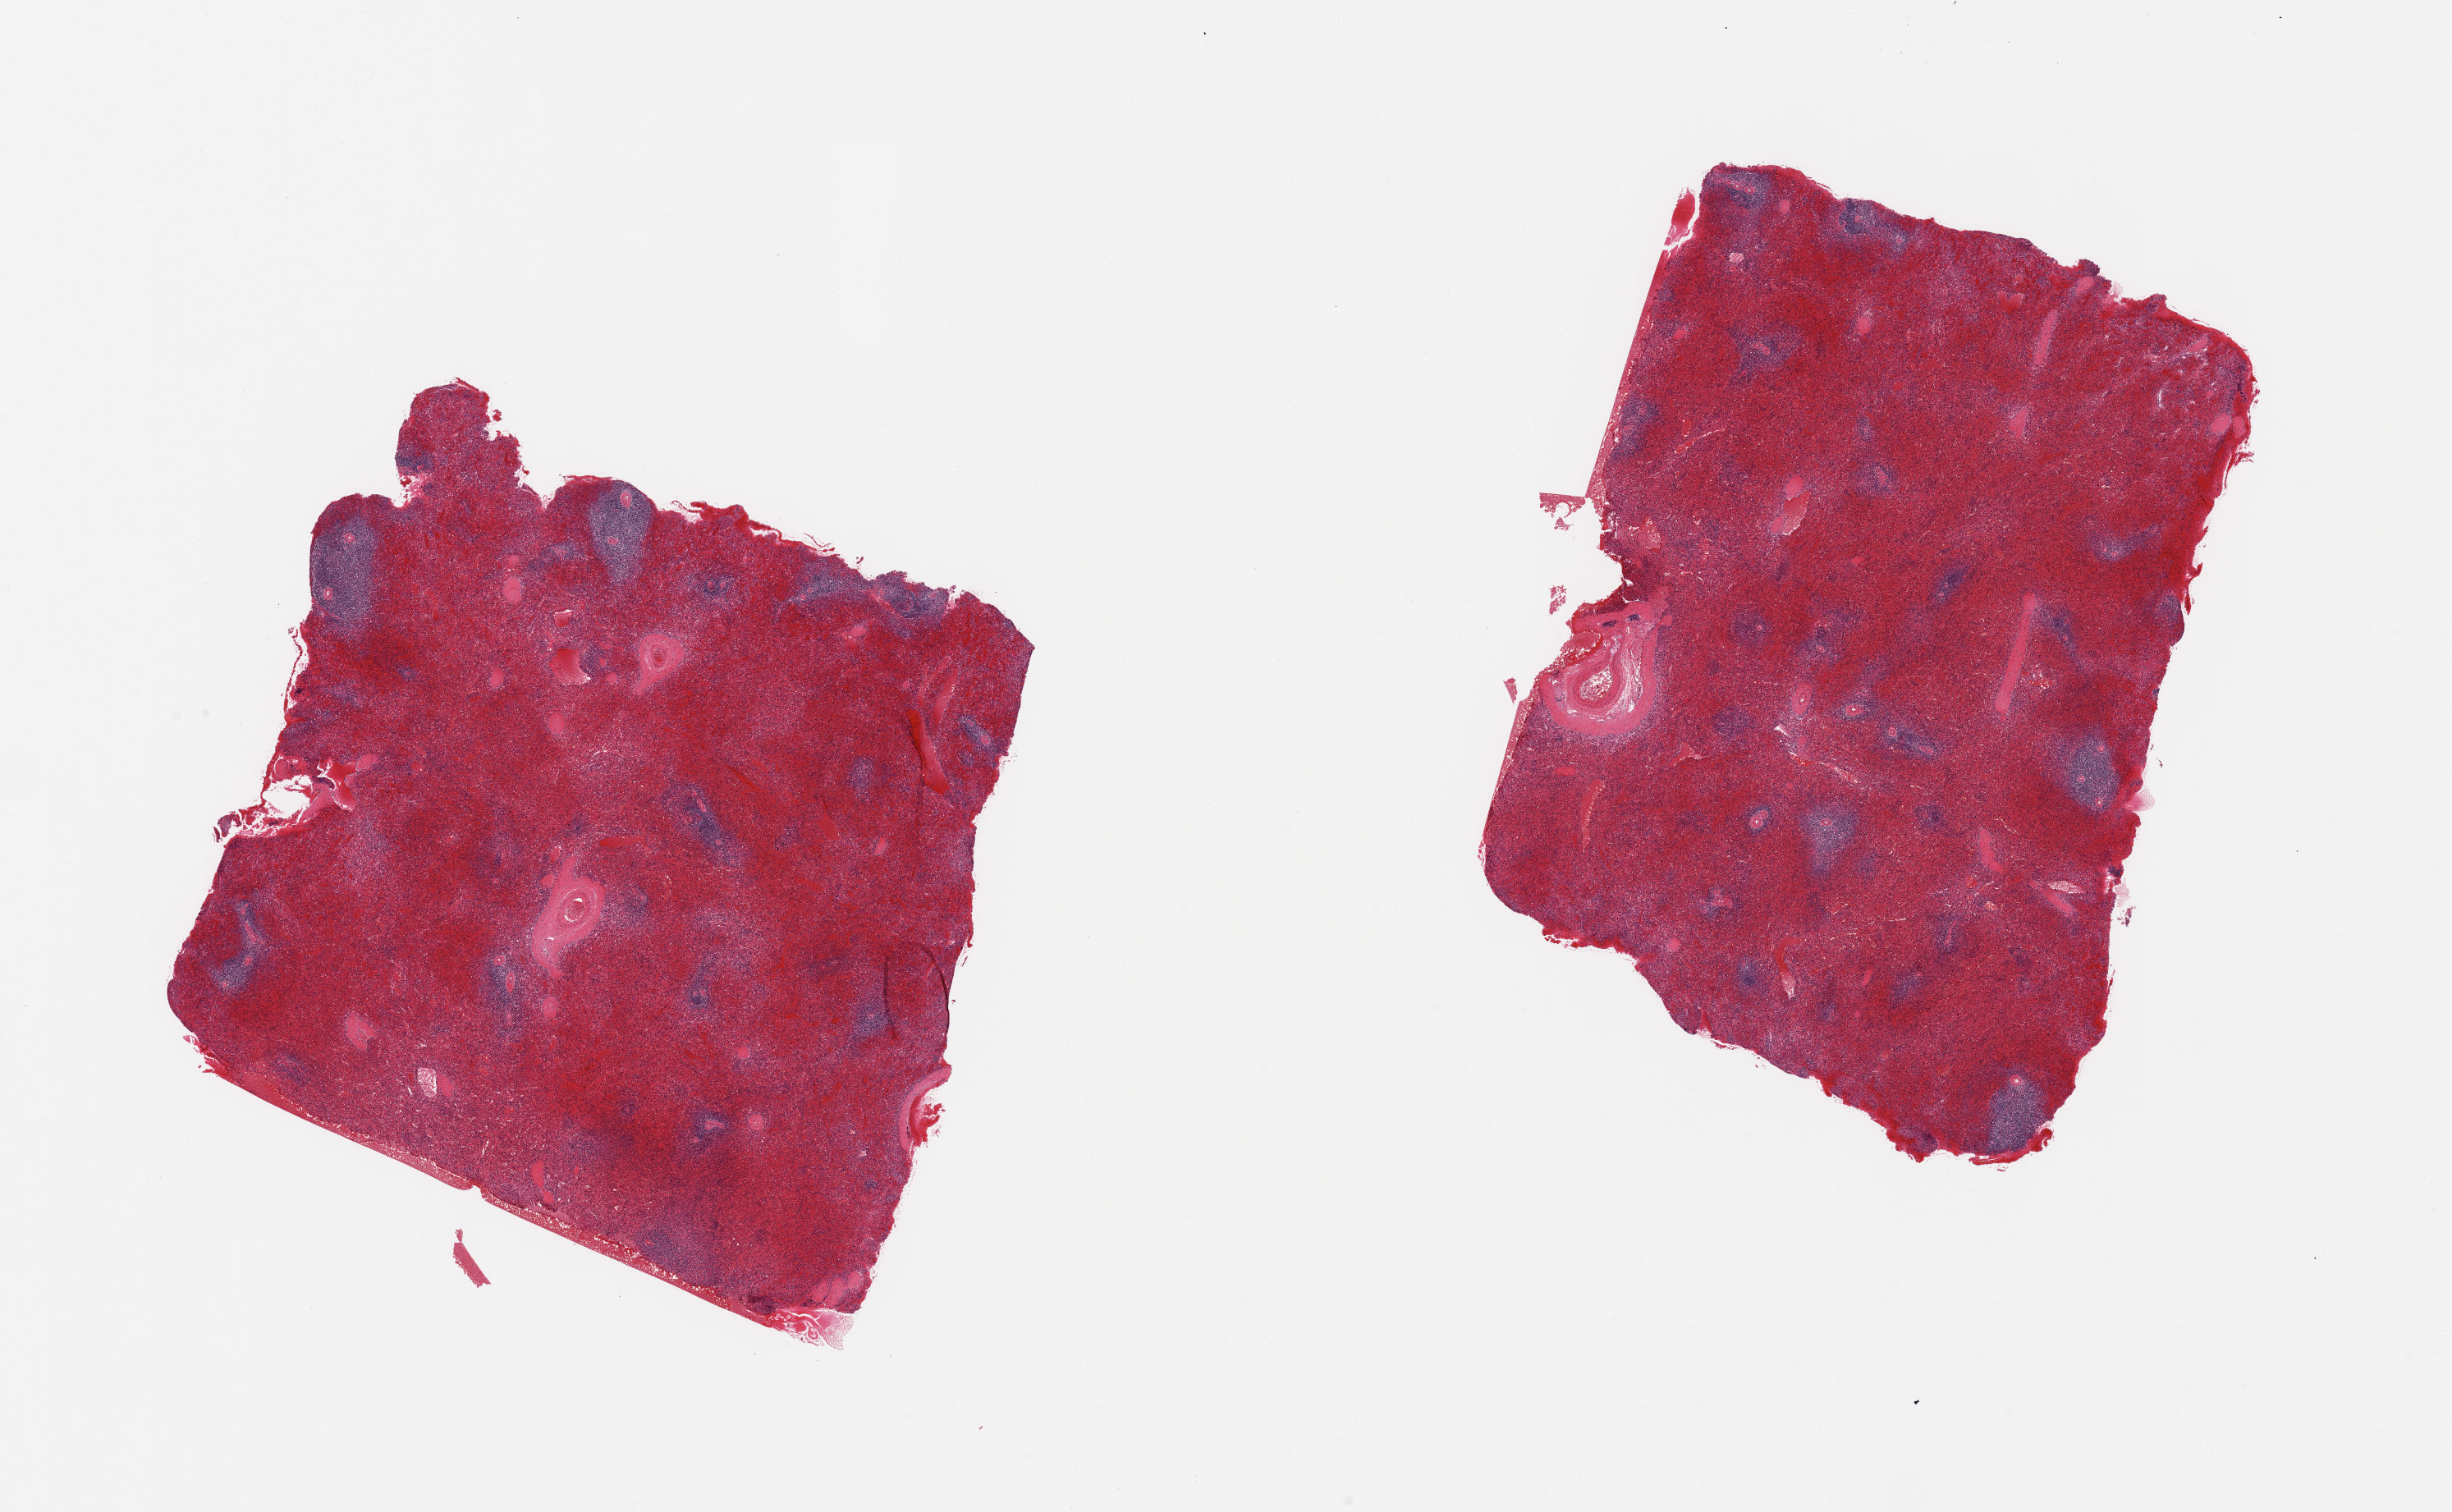
Whole-slide image, hematoxylin and eosin (H&E) stain, low-resolution overview of the scanned area, about 23.6 x 14.6 mm (from a 20x scan); PAXgene-fixed, paraffin-embedded tissue; sampled site (target tissue): spleen; tissue donor sample. Donor: male.
Review note (as recorded): 2 pieces, marked congestion.